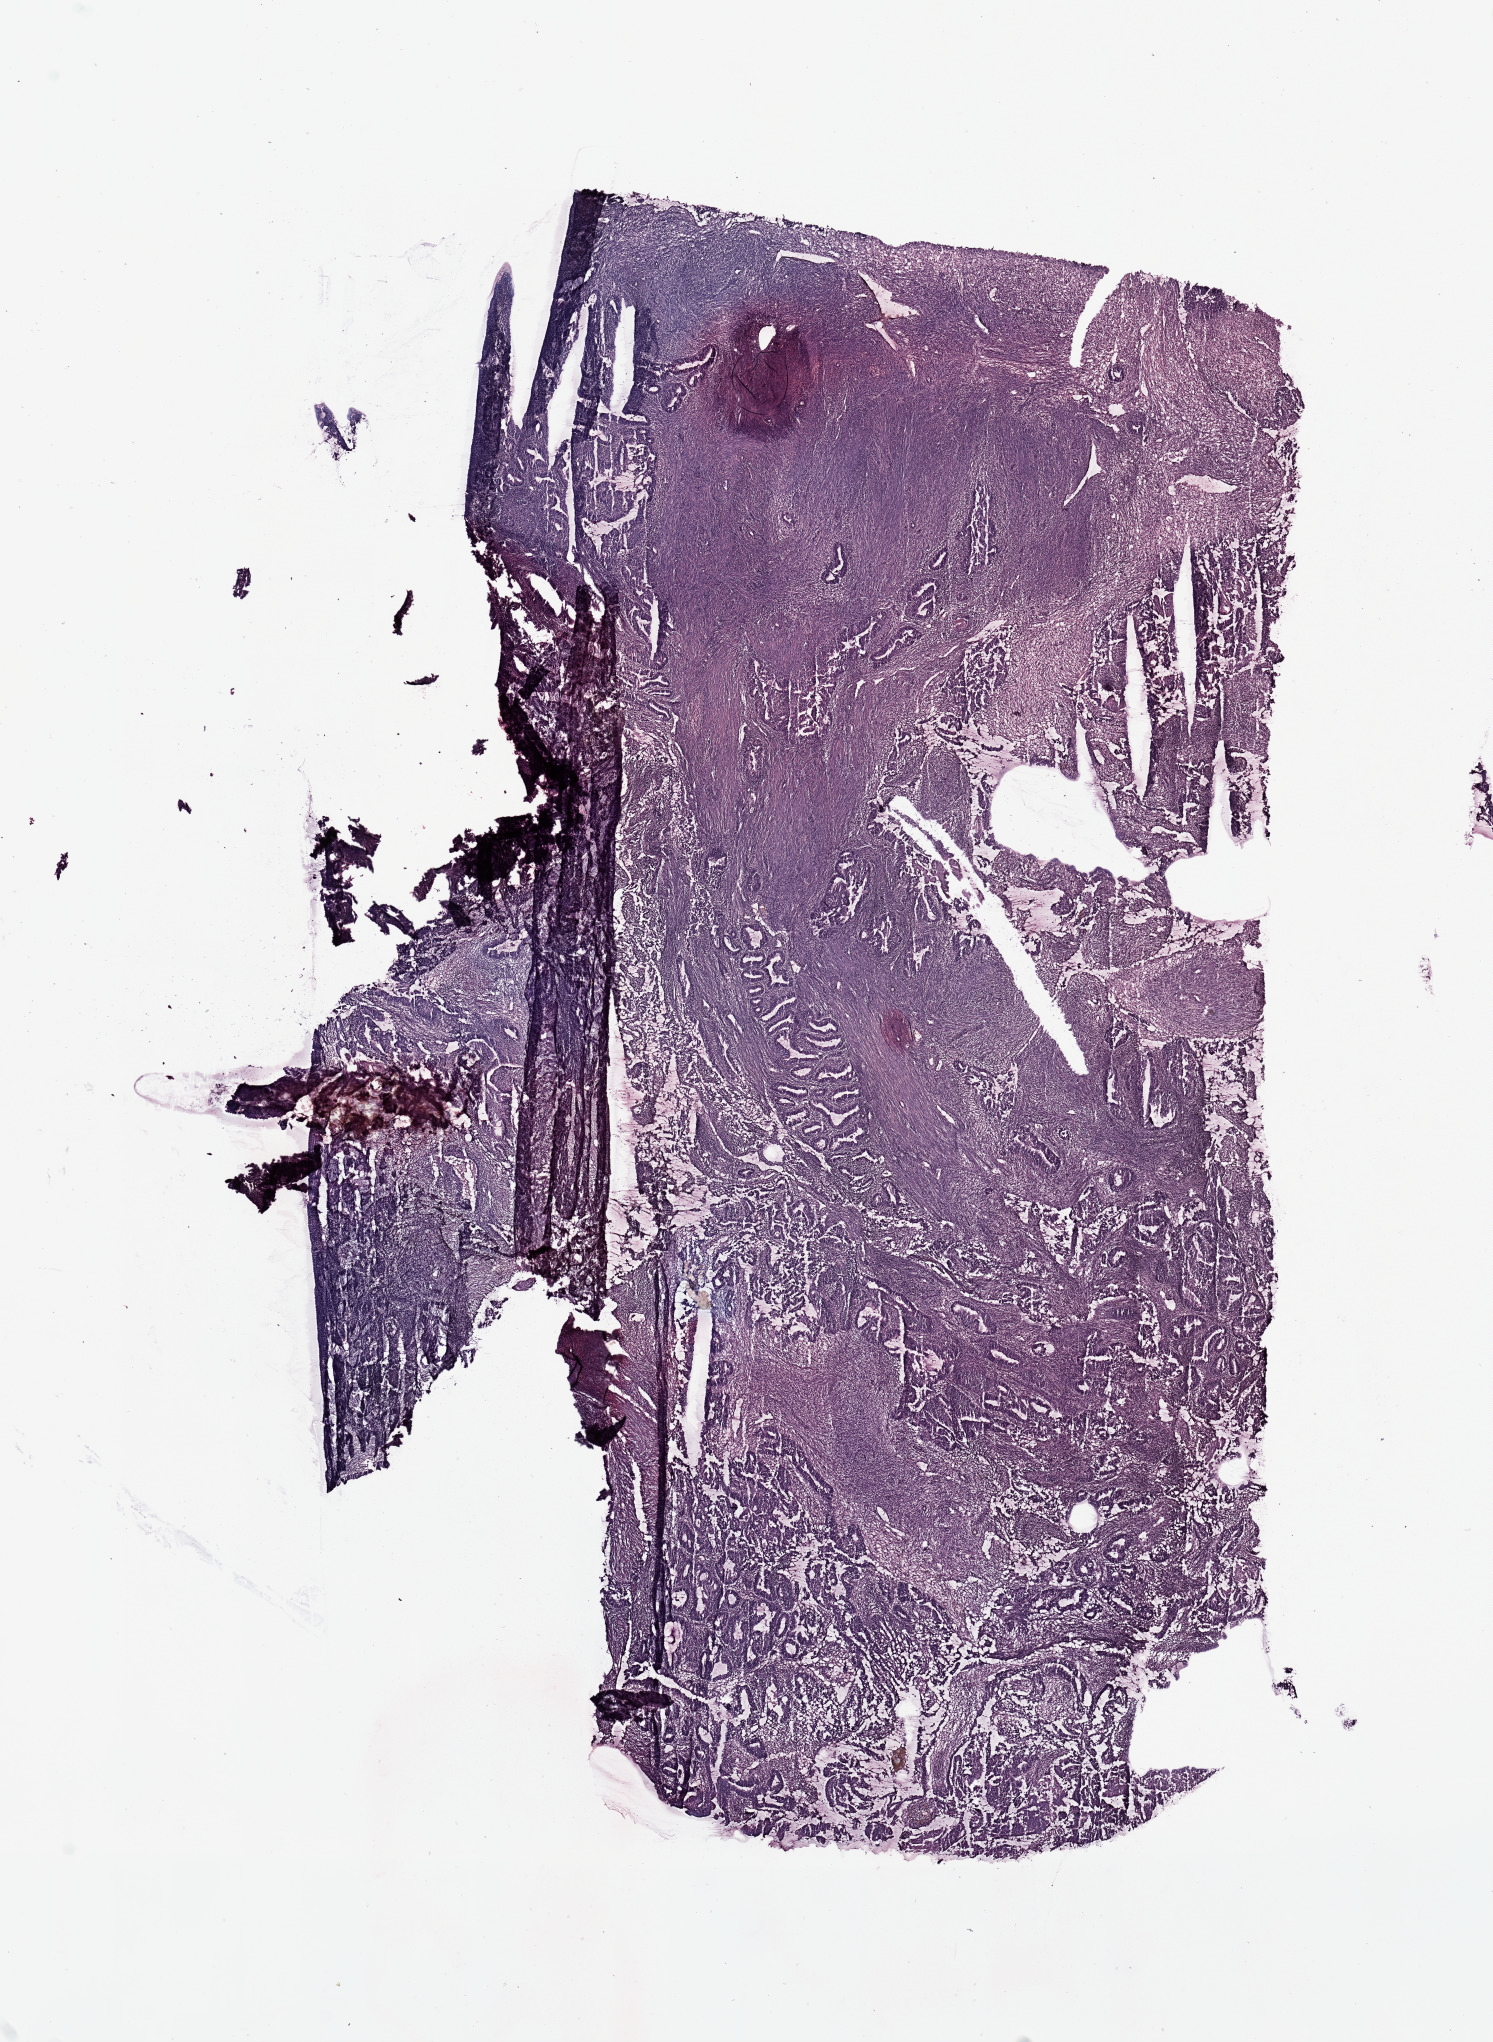
Digitized Hematoxylin and eosin (H&E) stained tissue section (whole slide) — whole scanned area (about 11.8 x 16.2 mm) shown as a low-resolution overview, uterus, tumour tissue. Female, 41 y/o.
Histologic diagnosis: Endometrioid adenocarcinoma, NOS.